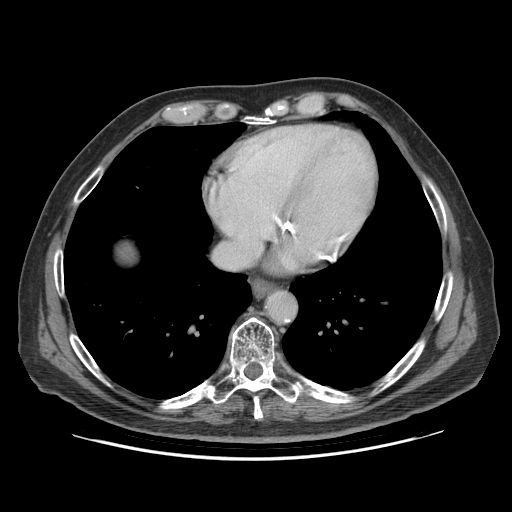
Contrast-enhanced abdominal CT (liver protocol), one axial slice. Slice 86 of 95 in the series (ordered by position). Reconstruction kernel STANDARD. 140 kVp. Soft-tissue window (W 400 / L 40 HU). 2.5 mm slice thickness. 512 × 512 image matrix. Case-level facts recorded for this patient, not image findings: diagnosis: hepatocellular carcinoma (patient treated with transarterial chemoembolisation; whether this scan precedes or follows treatment is not stated here); TNM stage (as recorded): Stage-IVB.
Structures marked on this image (semi-automatic segmentation, software-assisted and operator-edited):
- liver parenchyma outside the tumour (the mass and vessels are separate outlines, so this box may not span the whole liver): bounding box (x1, y1, x2, y2) in pixels: (118, 244, 134, 260)